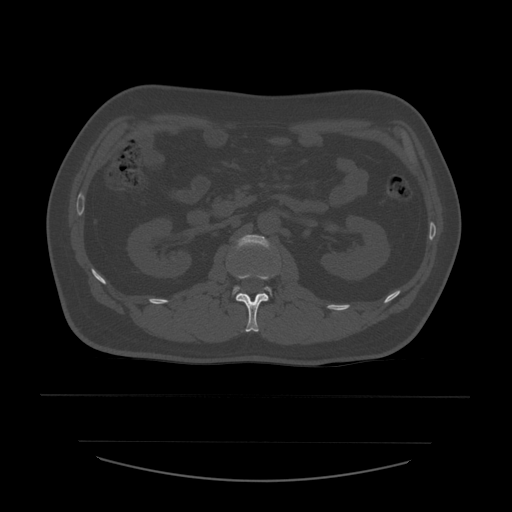
CT including the spine, one axial slice; slice 216 of 532 in the series (ordered by position); bone window (W 1800 / L 400 HU); 1.25 mm slice thickness; 512 × 512 image matrix, field of view 441 × 441 mm. Patient age 44 years. From the clinical record (not read from this slice): primary cancer: soft tissue sarcoma.
Annotated regions visible in this slice (semi-automatically segmented with operator editing):
- L1 vertebra: bounding box <236,273,276,332> (left, top, right, bottom; pixels)
- L2 vertebra: <233,235,272,295>